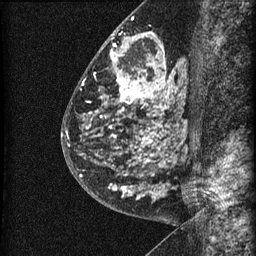
Breast MRI (dynamic contrast-enhanced), one sagittal slice. Dynamic contrast-enhanced series, image 2 of 3 at this slice position (ordered by acquisition). 1.5 T. TE 4.2 ms, TR 22.7 ms. 1.5 mm slice thickness. 256 × 256 image matrix, field of view 180 × 180 mm. Patient: female, 48 years. Case-level facts recorded for this patient, not image findings: setting: breast cancer imaged before/during neoadjuvant chemotherapy; receptor status: triple-negative.
Structures marked on this image (semi-automatically segmented with operator editing):
- analysis volume of interest (the breast-tissue region the enhancement analysis was run in; not a lesion): box from (x=81, y=23) to (x=186, y=202) px
- tumour enhancement mask (voxels above the 90 % enhancement threshold inside the analysis volume of interest): (x=81, y=33)–(x=175, y=198)